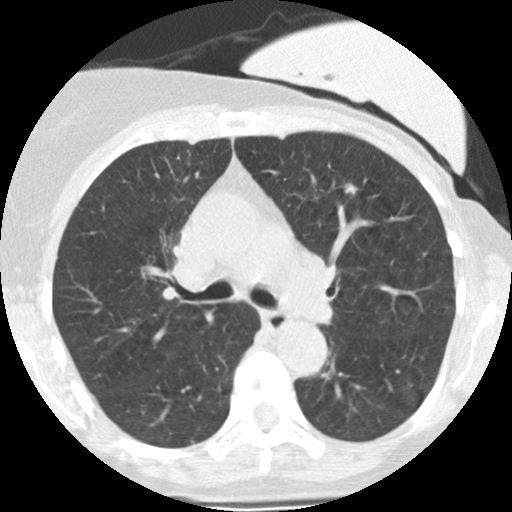
Low-dose screening chest CT, axial slice. Second screening round (one year after baseline). Lung window (W 1500 / L -600 HU). 2.5 mm slice thickness. Slice 93 of 251 in the series. Female participant, aged 66 years at enrolment. Former smoker at enrolment.
Lesion marked by an expert reader, bounding box <343,181,359,201> (left, top, right, bottom; pixels). Reader record for this screening exam (exam-level; its link to the box is not recorded): non-calcified nodule or mass ≥4 mm, left upper lobe, 7 × 5 mm, smooth margins, soft tissue attenuation, pre-existing on the prior screen: yes; interval growth: yes. Lung cancer was diagnosed 218 days after this screen: adenocarcinoma, NOS, left lower lobe, poorly differentiated (G3), stage IA (AJCC 6th edition), 8 mm at pathology.